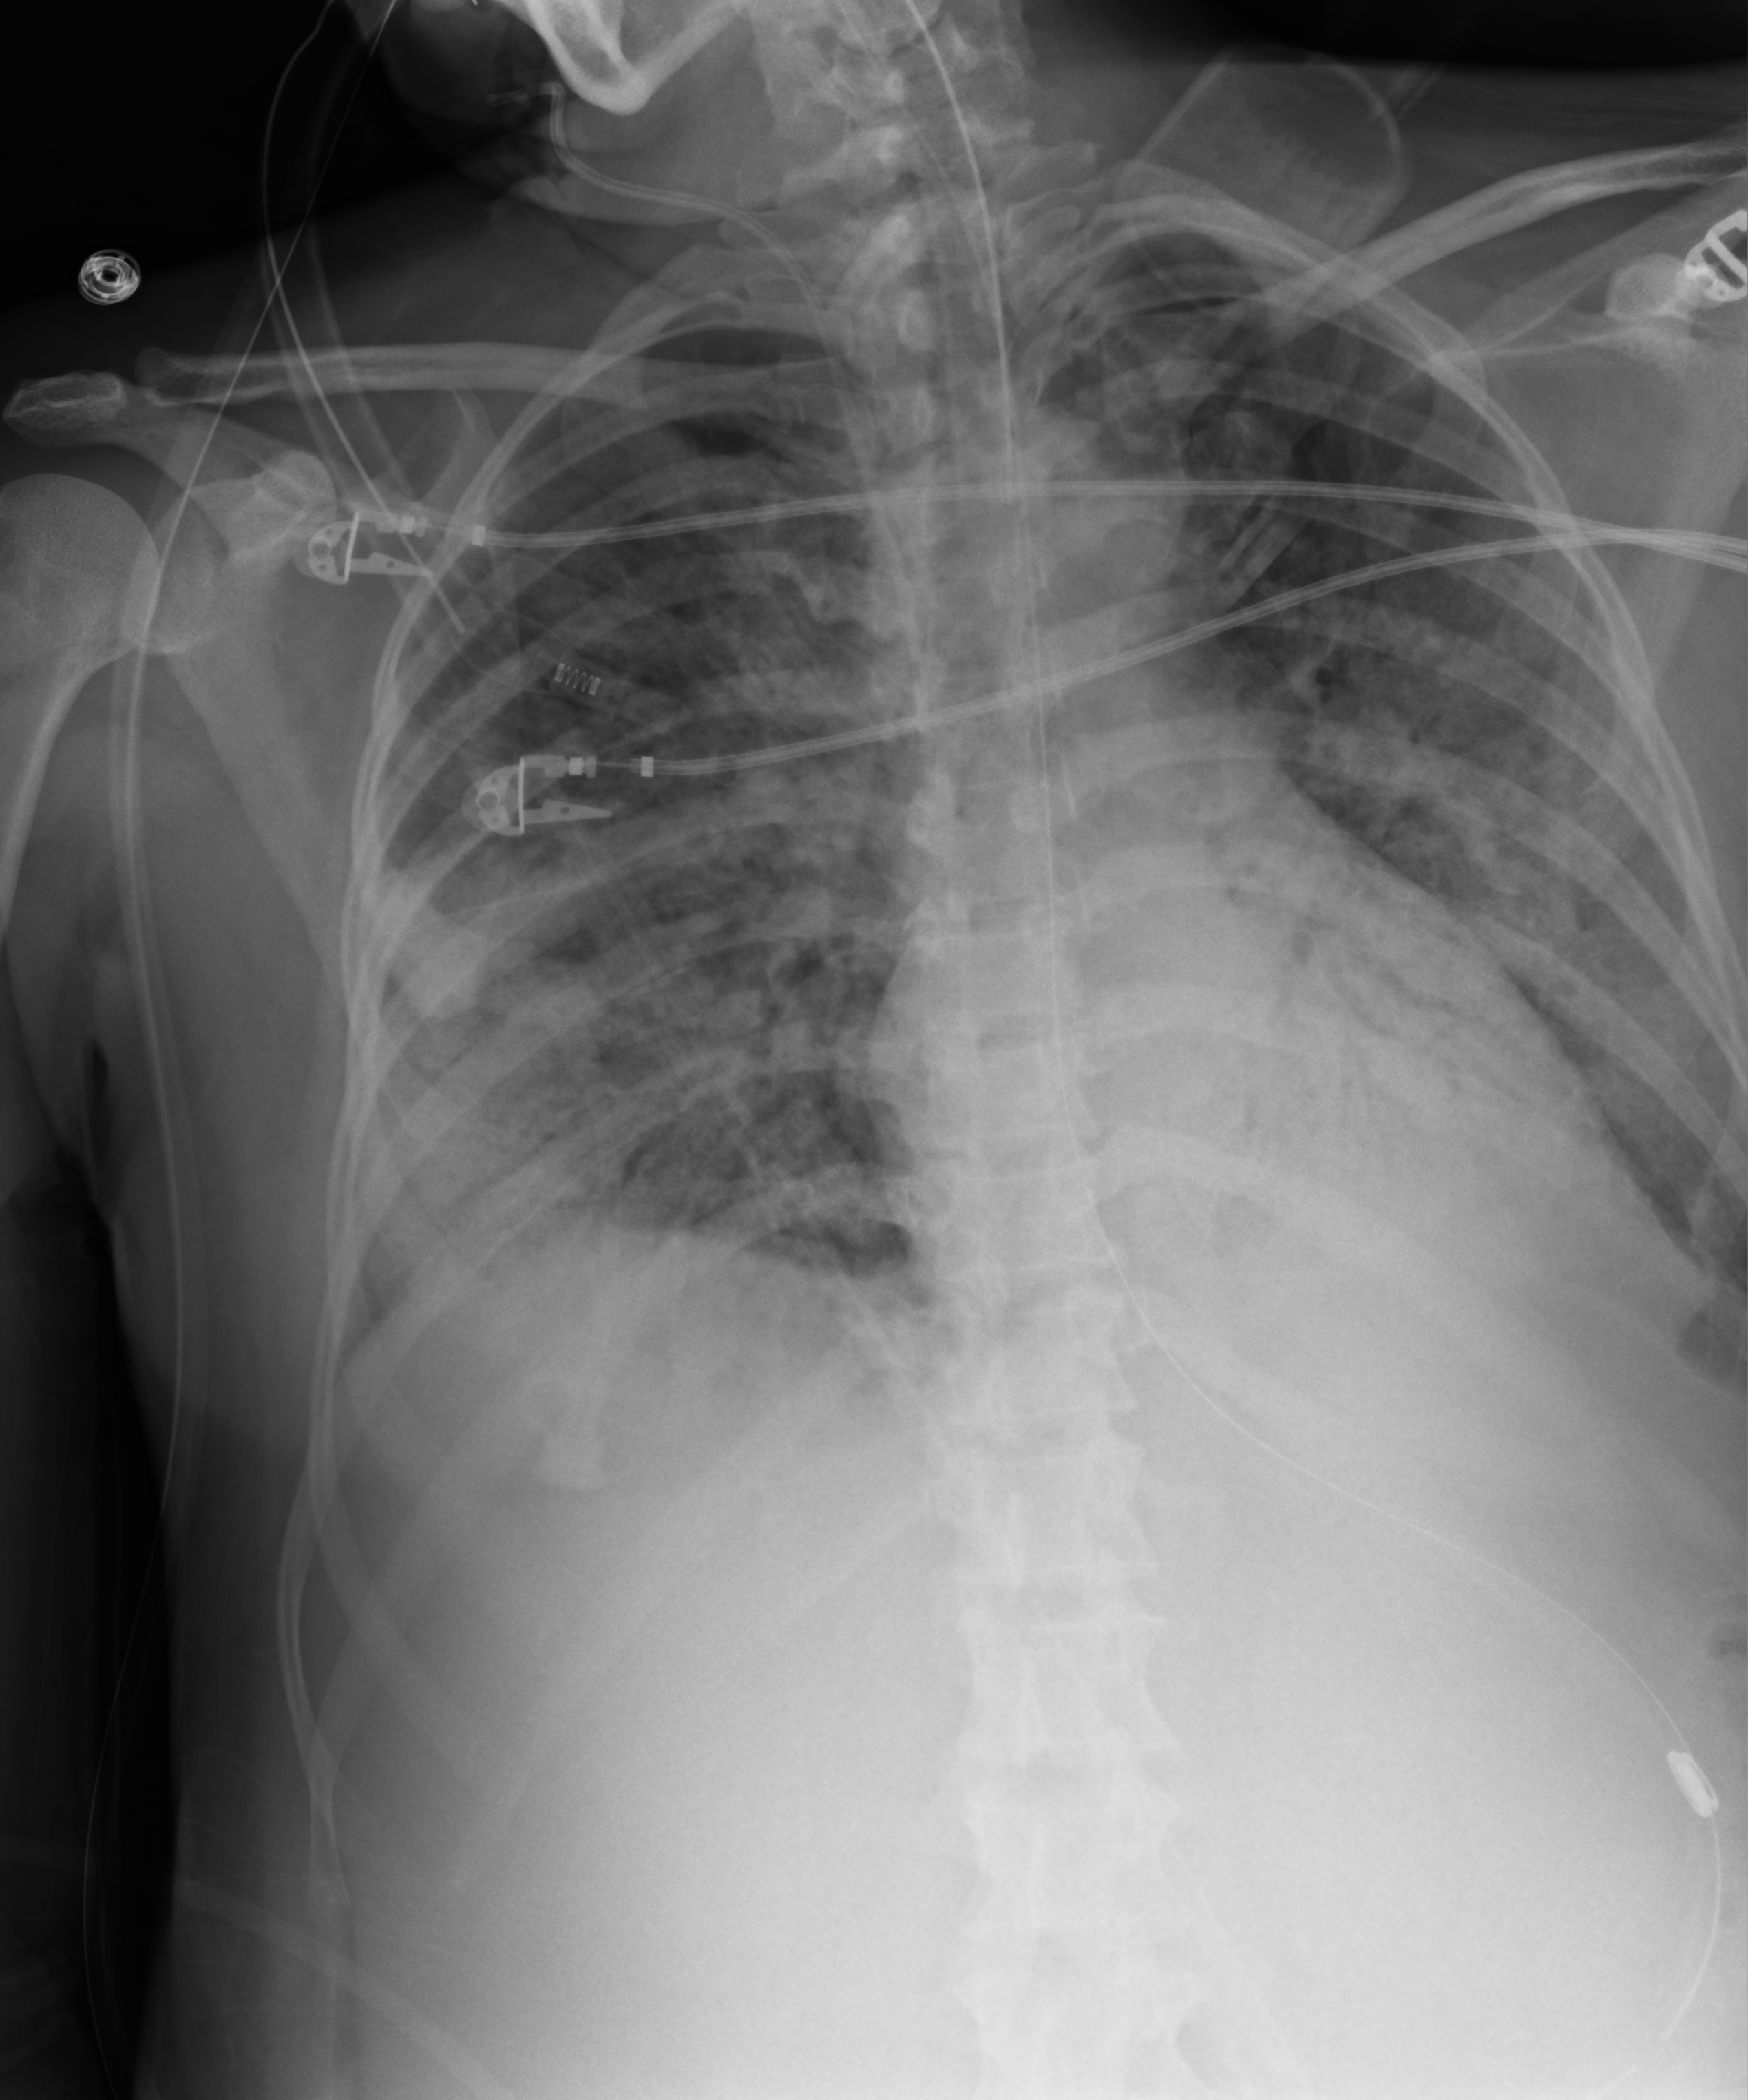
Portable chest radiograph, anteroposterior (AP) projection. Patient hospitalised with COVID-19; female, aged 18–59 years.
Hospital-stay facts (about this admission, not read from this image; timing relative to this image not recorded): mechanically ventilated during this hospital stay: yes.